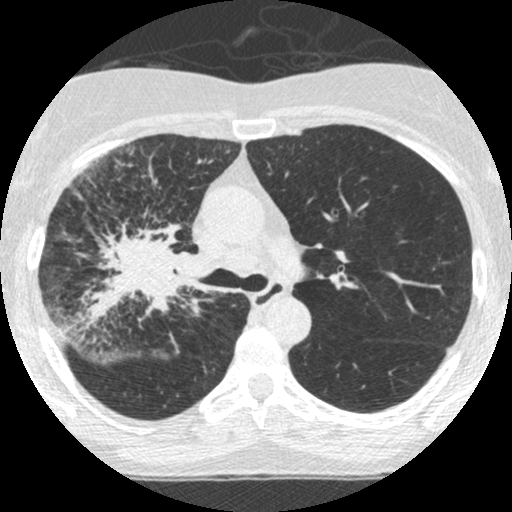
Low-dose screening chest CT, one axial slice; position 171 of 253 along the scan axis; 120 kVp; lung window (W 1500 / L -600 HU); 512 × 512 image matrix, field of view 294 × 294 mm.
Structures marked on this image (expert manual segmentation):
- lesion 2 (tumor, hilum of right lung): bounding box <77,214,202,325> (left, top, right, bottom; pixels)